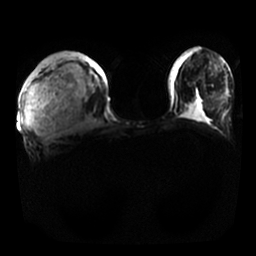
Breast MRI, one axial slice; position 6 of 25 along the scan axis; diffusion-weighted series; image 2 of 4 stored at this slice position (different b-values; order by instance number); 1.5 T; 4 mm slice thickness; 256 × 256 image matrix. Female patient.
Structures marked on this image (expert manual segmentation):
- tumour on diffusion-weighted imaging: bounding box (x1, y1, x2, y2) in pixels: (26, 66, 89, 135)